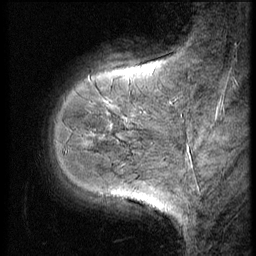
Breast MRI (dynamic contrast-enhanced), one sagittal slice. Slice 12 of 56 in the series (ordered by position). 3 images stored at this slice position (order not interpretable as contrast timing). 1.5 T. TE 4.2 ms, TR 9 ms. 2.5 mm slice thickness. 256 × 256 image matrix, field of view 180 × 180 mm. Patient: female, 49 years. Case-level facts recorded for this patient, not image findings: setting: breast cancer imaged before/during neoadjuvant chemotherapy; receptor status: HER2-positive.
Annotated regions visible in this slice (semi-automatic segmentation, software-assisted and operator-edited):
- analysis volume of interest (the breast-tissue region the enhancement analysis was run in; not a lesion): bounding box (x1, y1, x2, y2) in pixels: (40, 74, 148, 198)
- tumour enhancement mask (voxels above the 140 % enhancement threshold inside the analysis volume of interest): (100, 136, 104, 140)